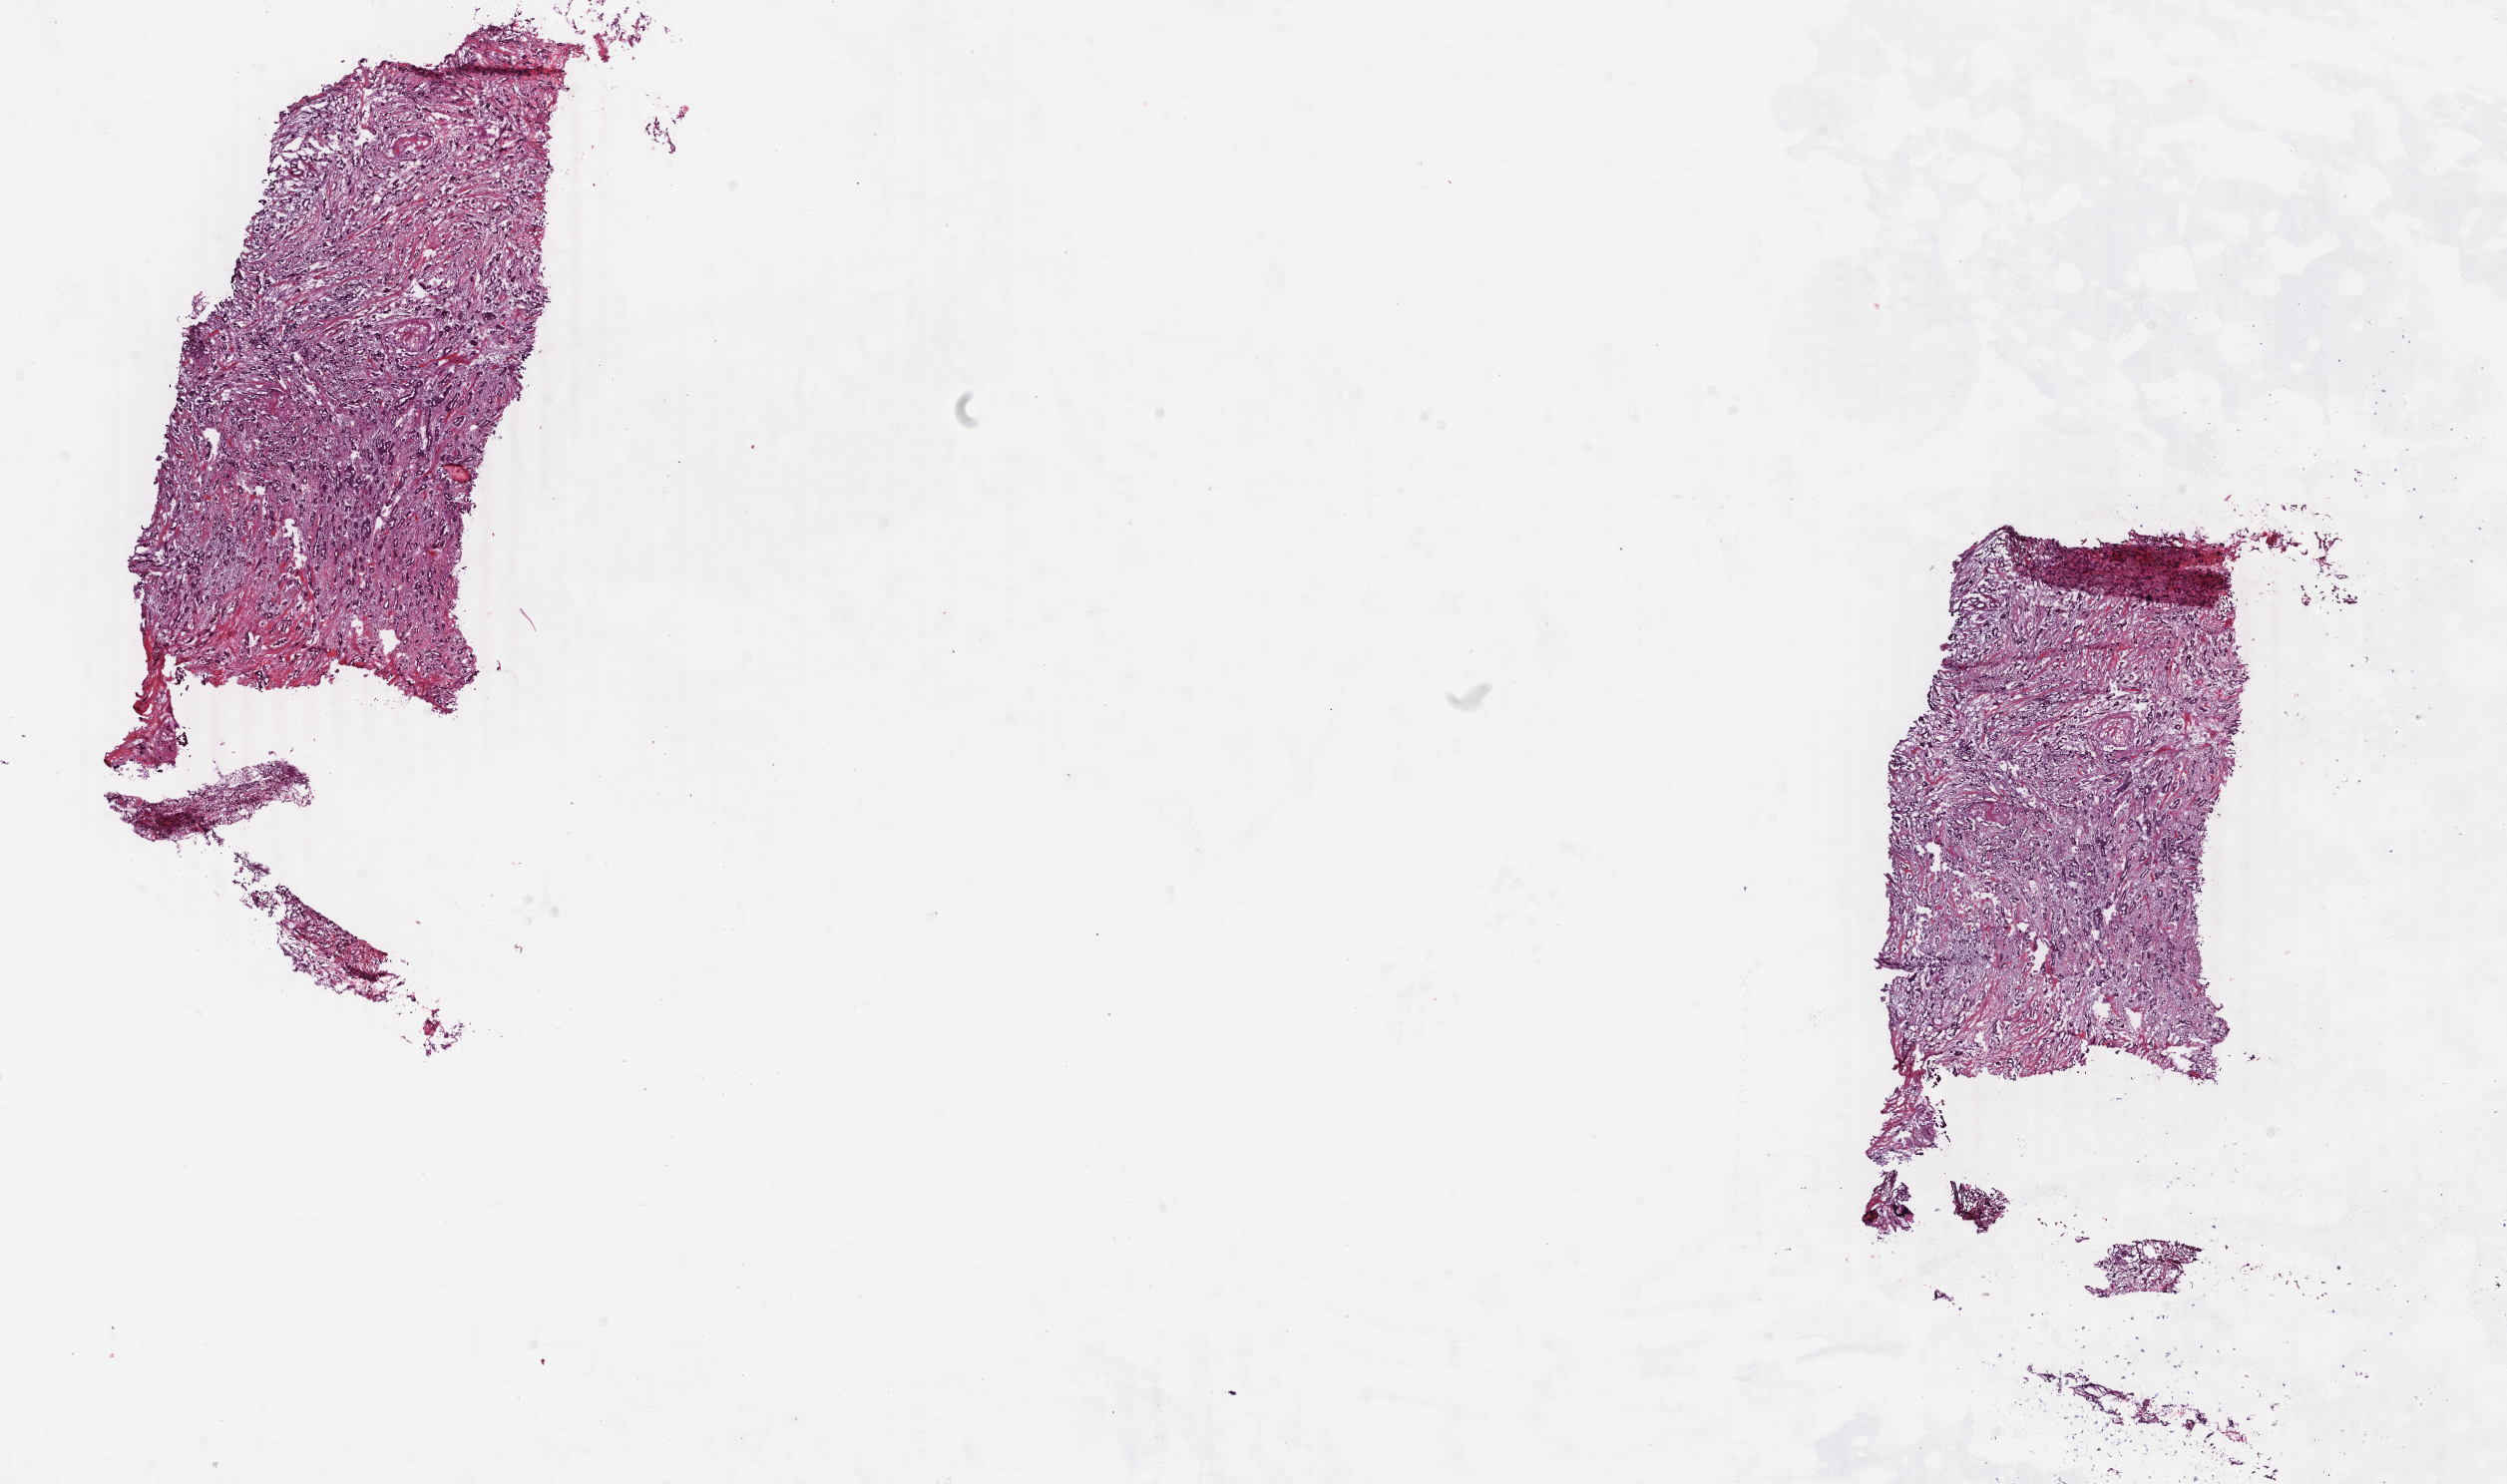
H&E whole-slide image — low-resolution overview of the scanned area, about 20.0 x 11.8 mm; frozen section; breast, primary tumour sample. Female patient; age at initial diagnosis 66 years. Pathologist review of this section (percent, as recorded): tumour cells 75%, tumour nuclei 75%, normal cells 0%, stromal cells 23%, necrosis 2%. Infiltration values recorded for this section: lymphocyte infiltration 1%, monocyte infiltration 0%, neutrophil infiltration 0%.
Diagnosis: Infiltrating duct carcinoma, NOS. AJCC pathologic stage: IA. Lymph nodes positive (case pathology): 0 of 6 examined.